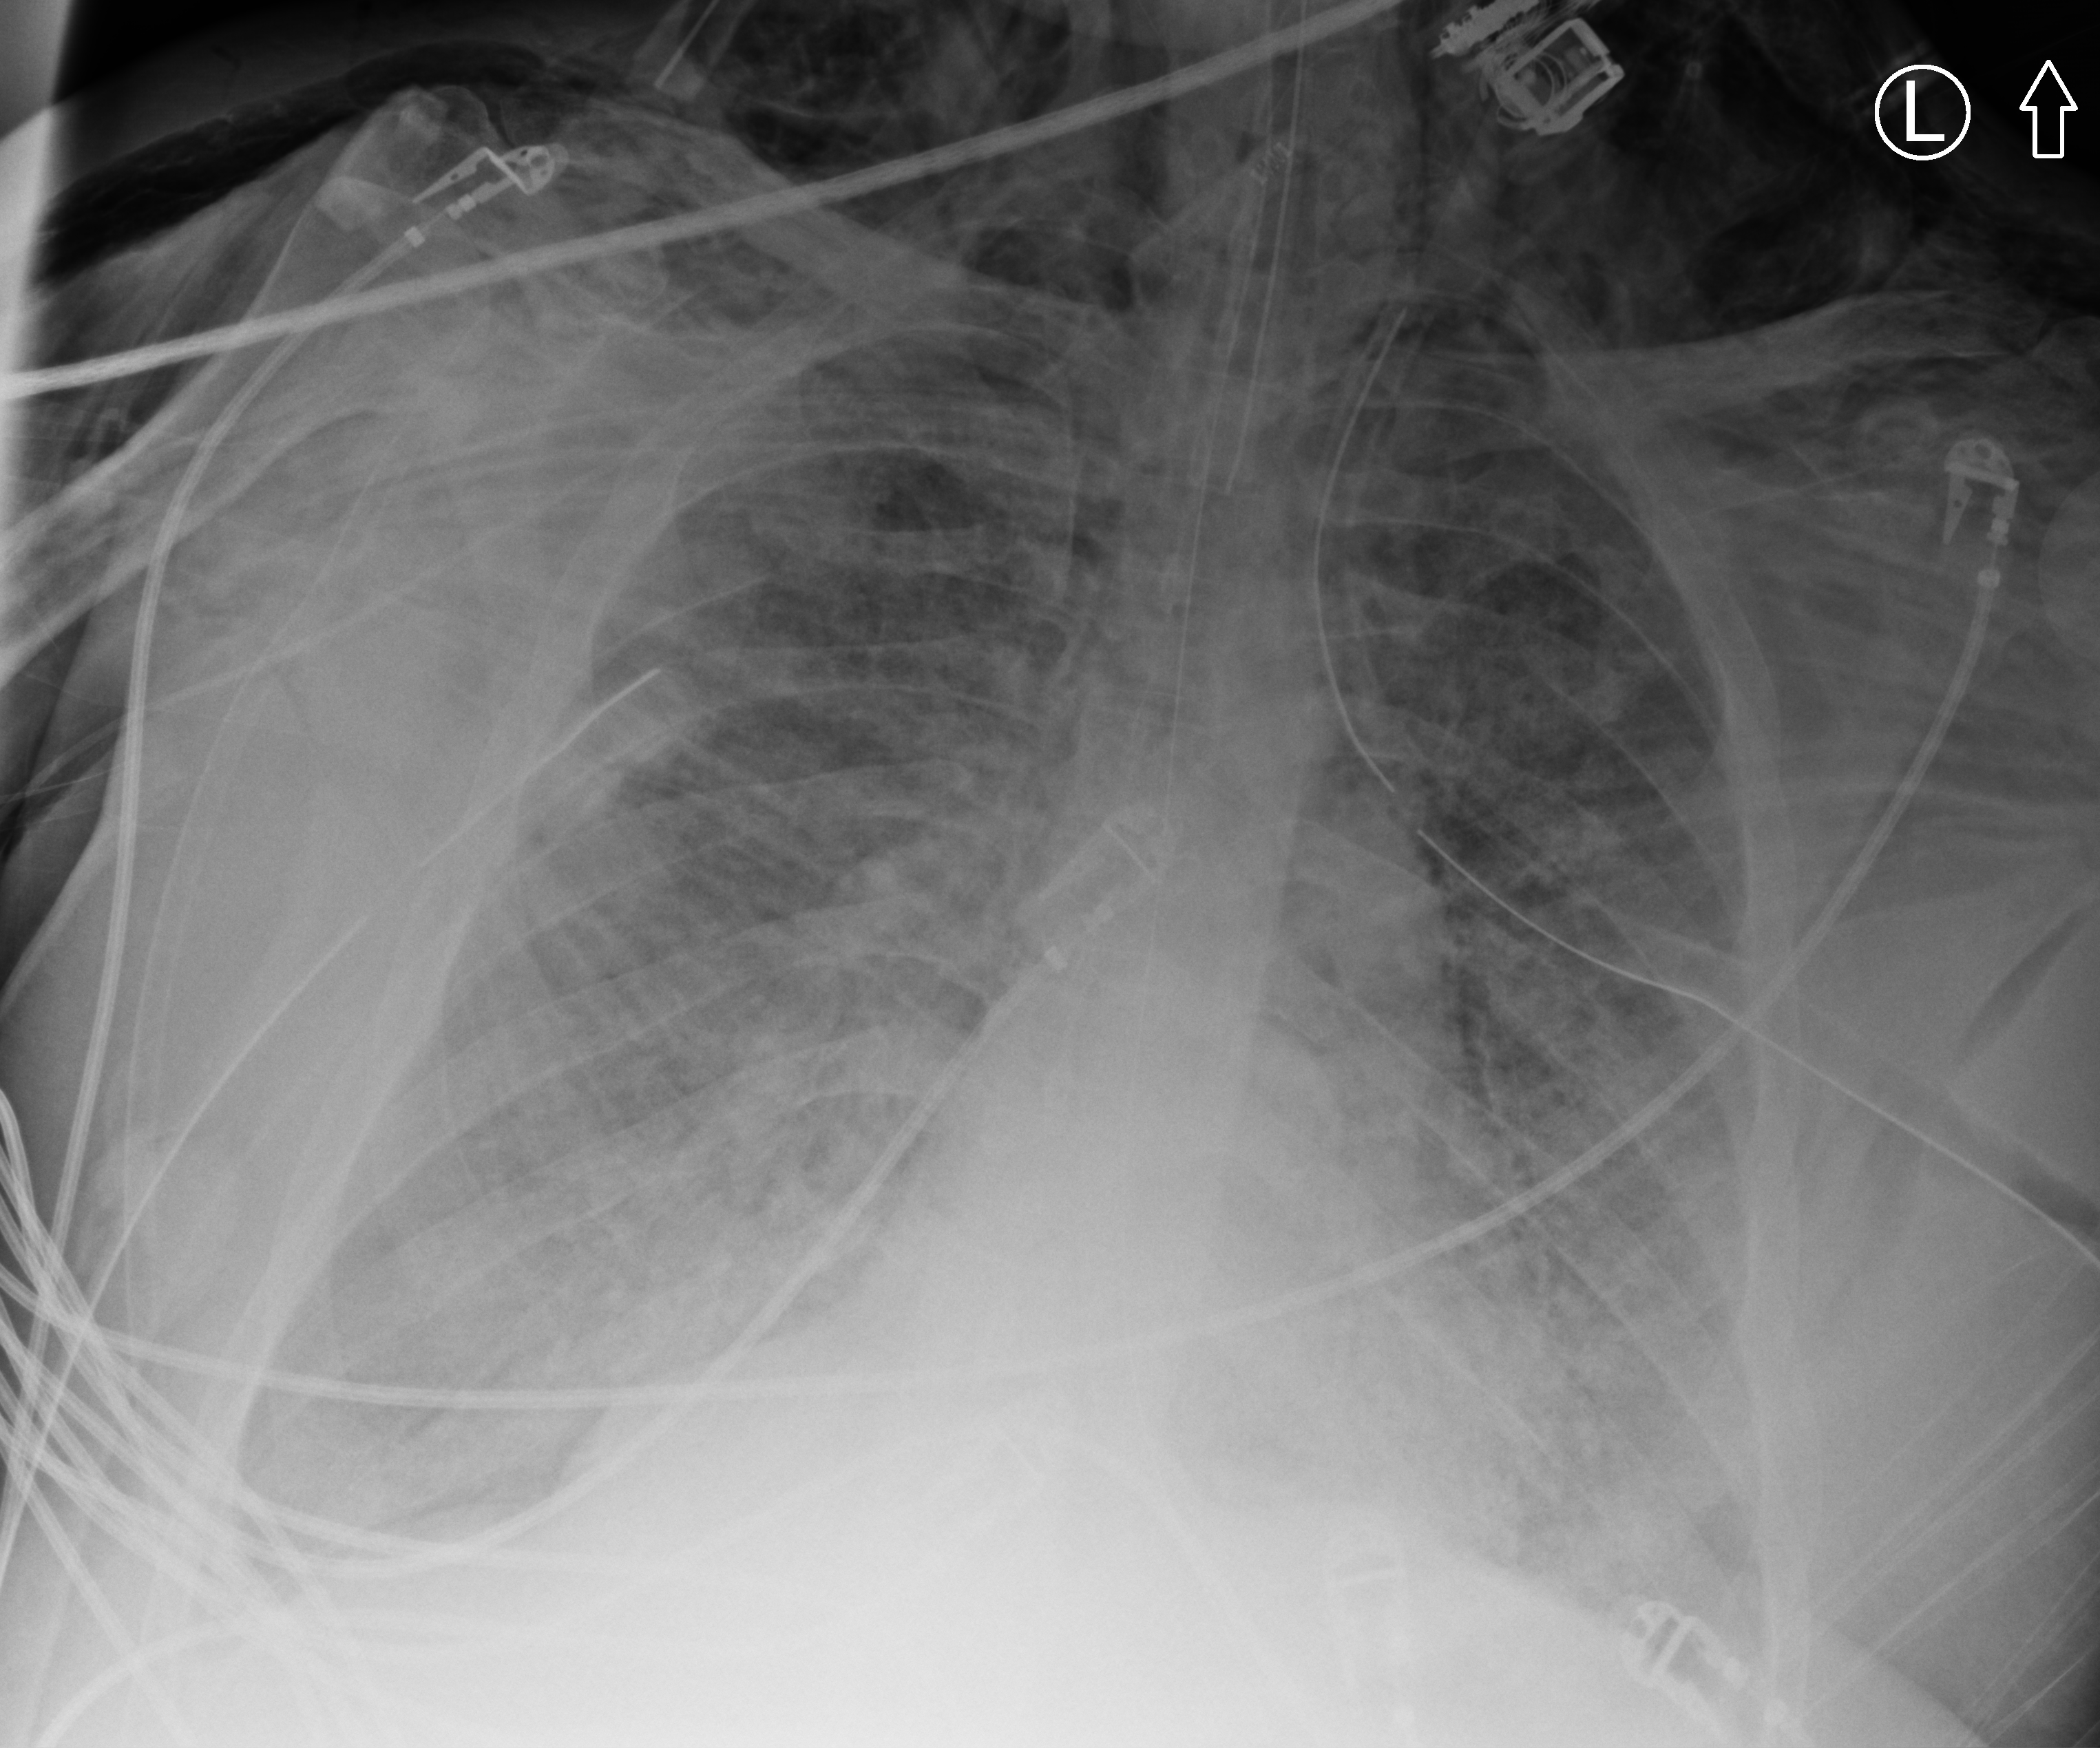
Chest X-ray (portable), anteroposterior (AP) projection. Patient hospitalised with COVID-19, aged 18–59 years.
Admission-level facts for this patient (not findings on this image; timing relative to this image not recorded): other chronic lung disease (admission record): no; mechanically ventilated during this hospital stay: yes; length of hospital stay: 15 days.